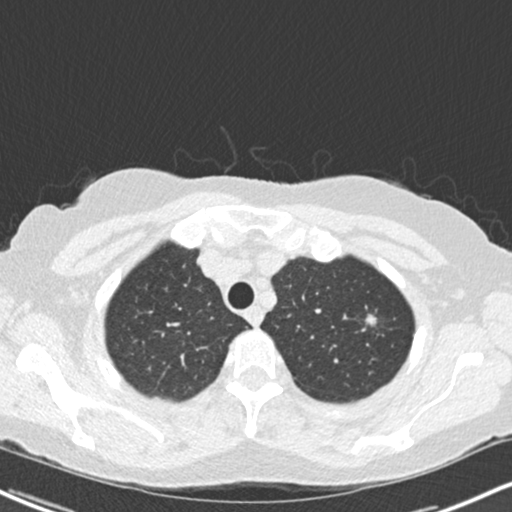
Low-dose screening chest CT, axial slice; baseline screening round; lung window (W 1500 / L -600 HU); 2 mm slice thickness. Female participant, aged 64 years at enrolment.
Expert-annotated lung lesion, bounding box (x1, y1, x2, y2) in pixels: (358, 307, 390, 338). The screening reader recorded 2 non-calcified nodules or masses ≥4 mm on this exam (left upper lobe, lingula); which of them this box marks is not recorded. Later outcome: lung cancer diagnosed 477 days after this screen (after the second annual screen) — signet ring cell carcinoma, right upper lobe, poorly differentiated (G3), stage IA (AJCC 6th edition), 15 mm at pathology.